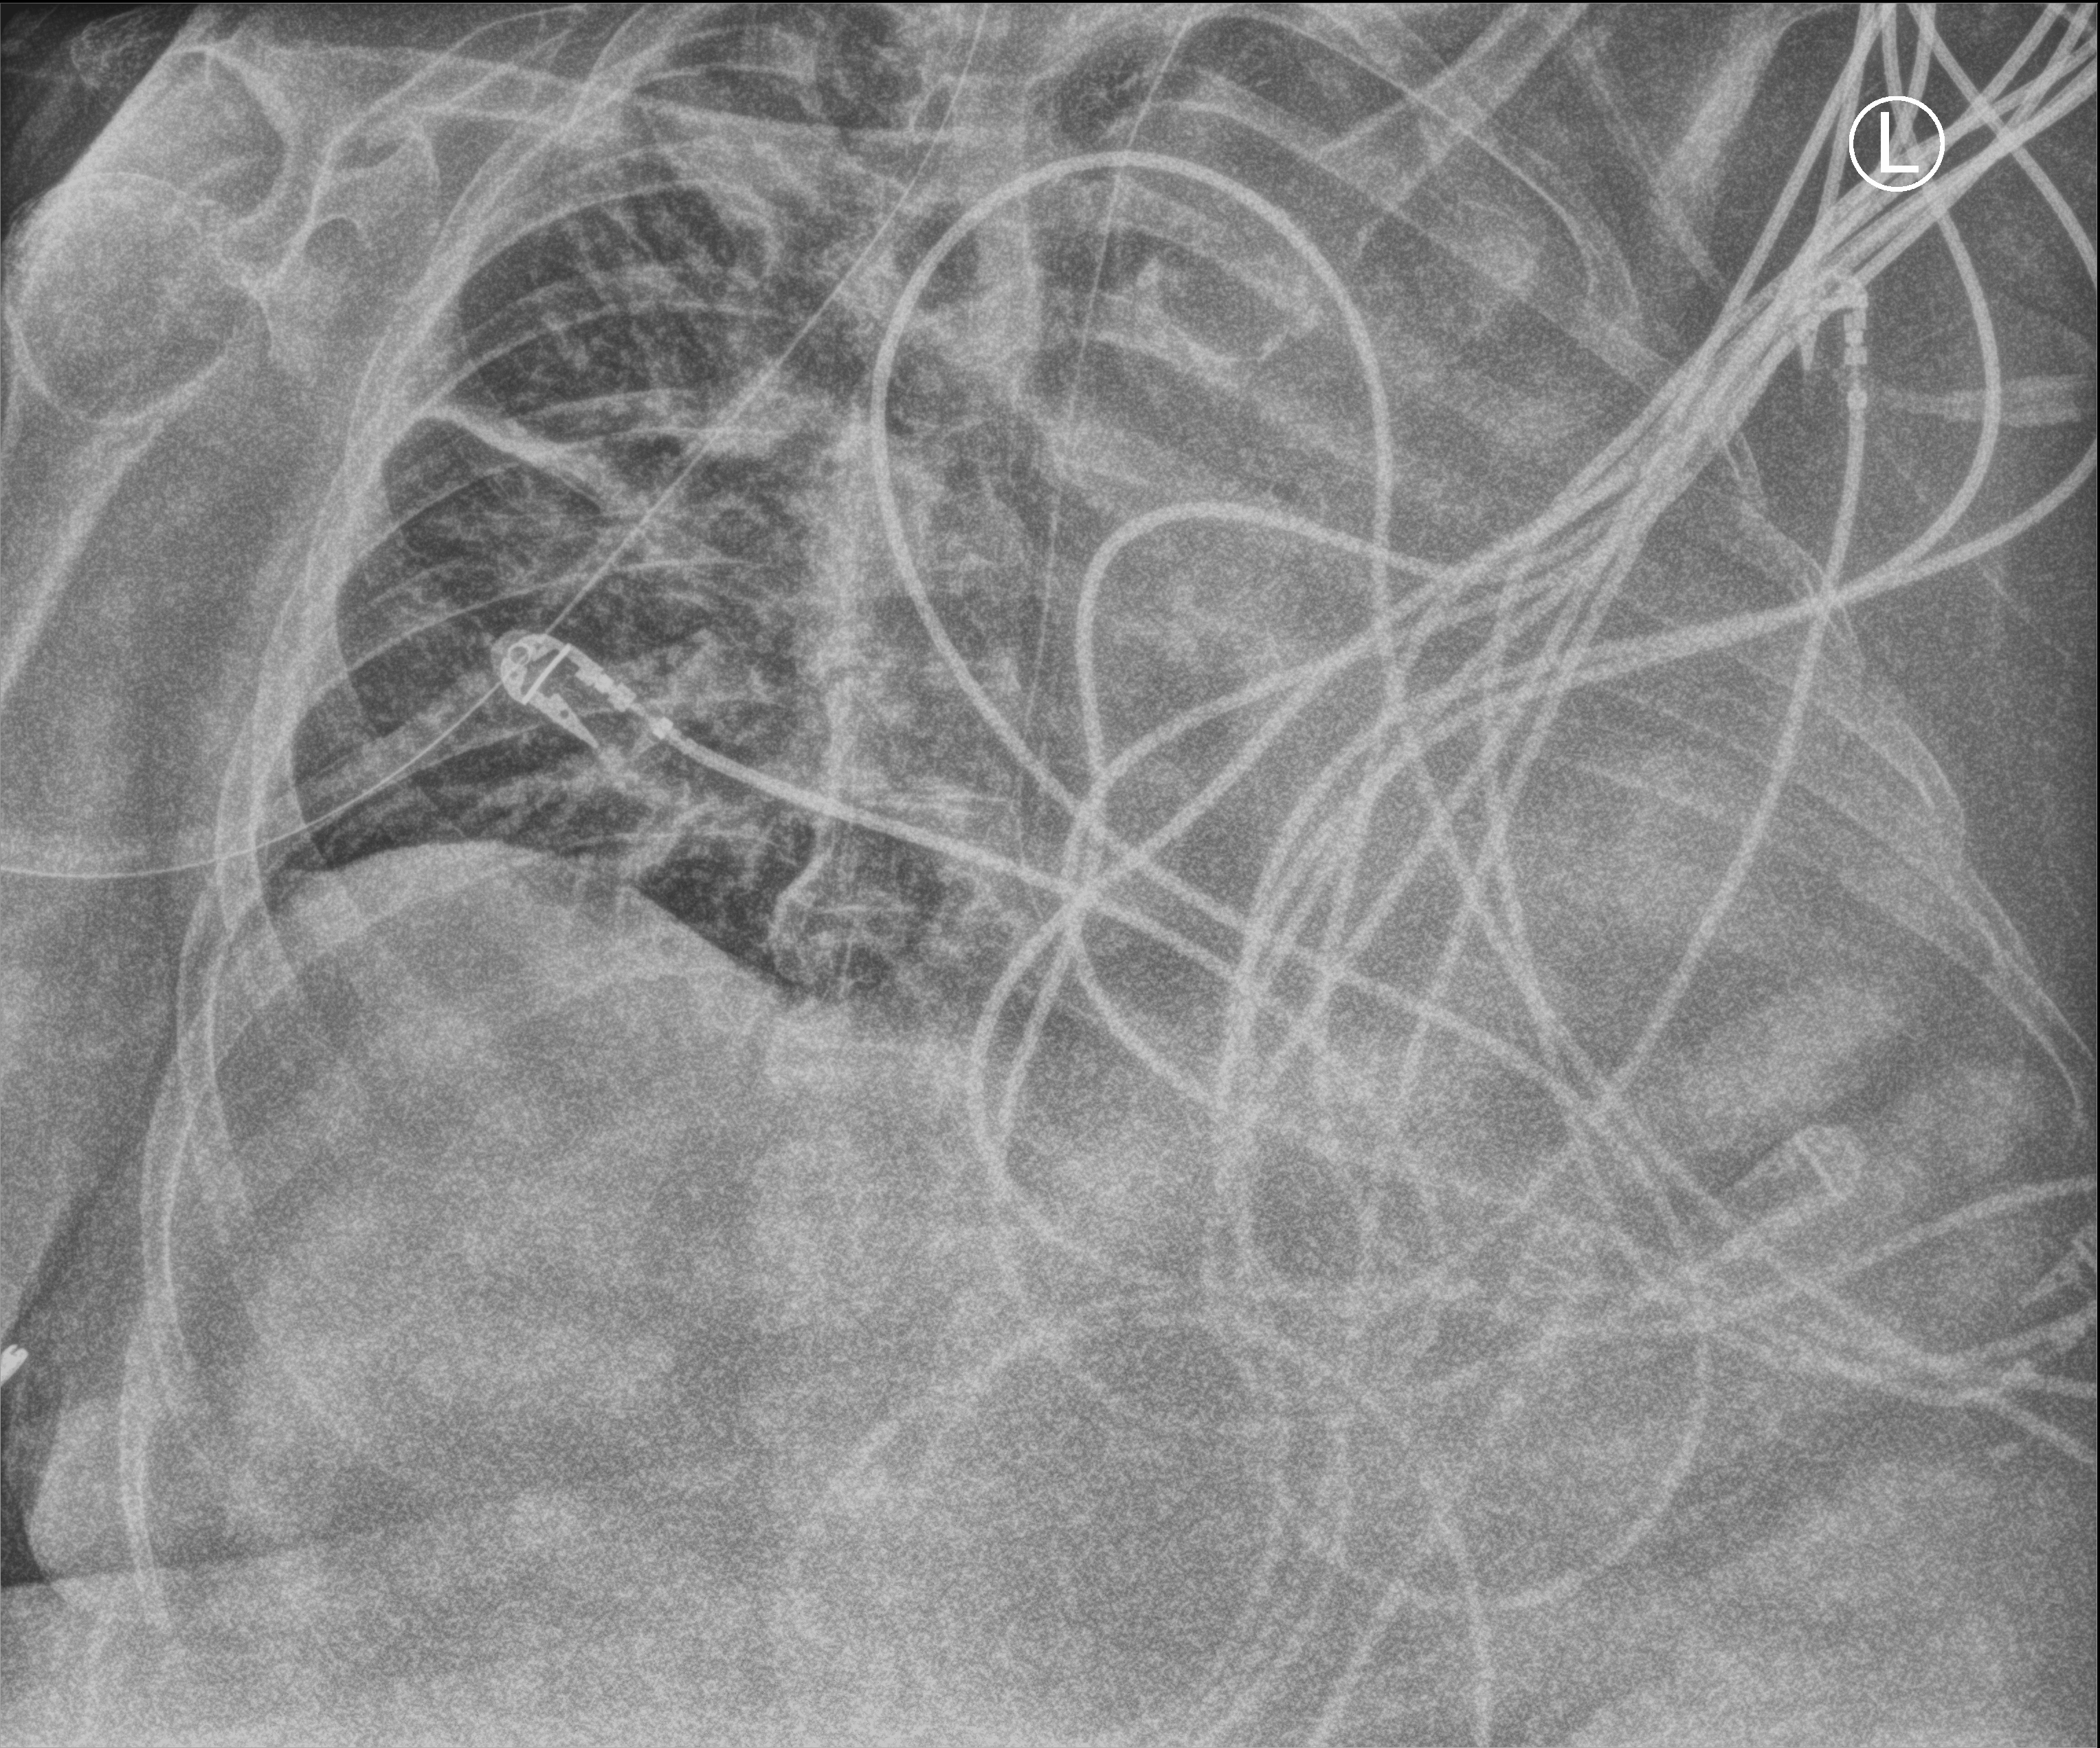
Portable chest radiograph. Female patient hospitalised with COVID-19, age 75–90 years.
Hospital-stay facts (about this admission, not read from this image; timing relative to this image not recorded): mechanically ventilated during this hospital stay: no.